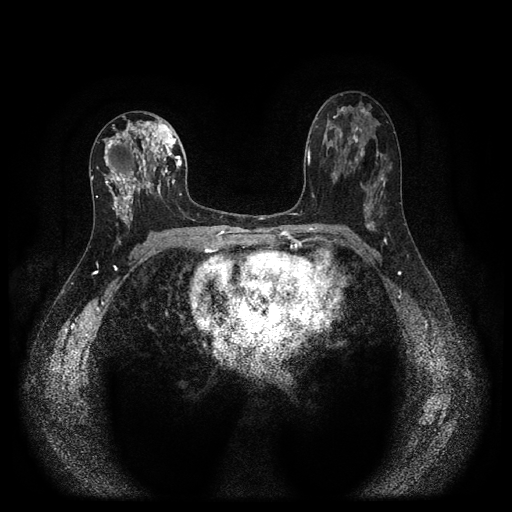
Breast MRI (dynamic contrast-enhanced, multi-phase), one axial slice. Slice 56 of 116 in the series (ordered by position). Dynamic contrast-enhanced series, time point 2 of 5 at this slice position (early post-contrast). 1.5 T. TE 2.7 ms, TR 5.4 ms. 2 mm slice thickness. 512 × 512 image matrix, field of view 330 × 330 mm. Patient: female, 47 years.
Structures marked on this image (semi-automatically segmented with operator editing):
- breast lesion (labelled 'tumour' in the annotation; benign lesions carry a separate 'benign' label): bounding box [x1, y1, x2, y2] px = [96, 120, 182, 235]